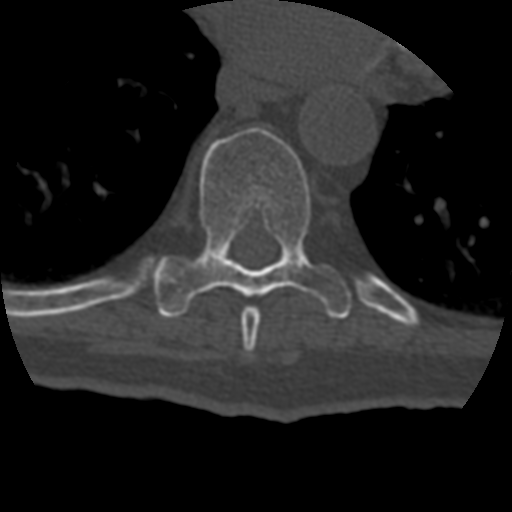
CT including the spine, one axial slice; slice 242 of 399 in the series (ordered by position); 120 kVp; bone window (W 1800 / L 400 HU); 1.25 mm slice thickness; 512 × 512 image matrix, field of view 160 × 160 mm. Patient age 69 years. Case-level facts recorded for this patient, not image findings: primary cancer: prostate.
Annotated regions visible in this slice (semi-automatically segmented with operator editing):
- T8 vertebra: box from (x=241, y=306) to (x=261, y=352) px
- T9 vertebra: (x=148, y=127)–(x=352, y=319)